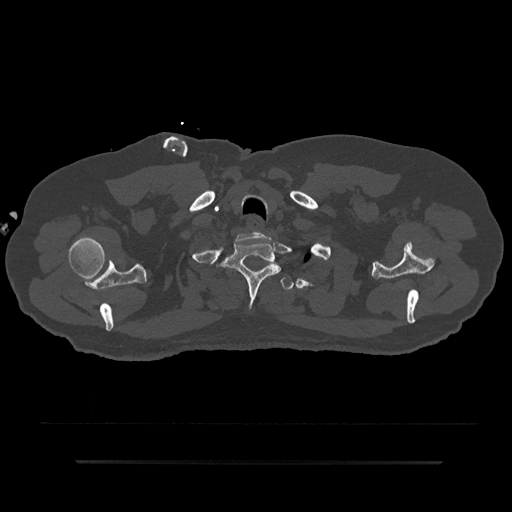
CT including the spine, one axial slice. Position 734 of 797 along the scan axis. Reconstruction kernel Br40s/3. 120 kVp. Bone window (W 1800 / L 400 HU). 0.5 mm slice thickness. 512 × 512 image matrix, field of view 464 × 464 mm. Patient: male, 59 years. From the clinical record (not read from this slice): primary cancer: bile ducts; vertebrae with lytic lesions (as recorded): T10.
Outlined on this slice (semi-automatic segmentation, software-assisted and operator-edited):
- T1 vertebra: bounding box (x1, y1, x2, y2) in pixels: (222, 238, 281, 308)
- T2 vertebra: (277, 264, 294, 290)